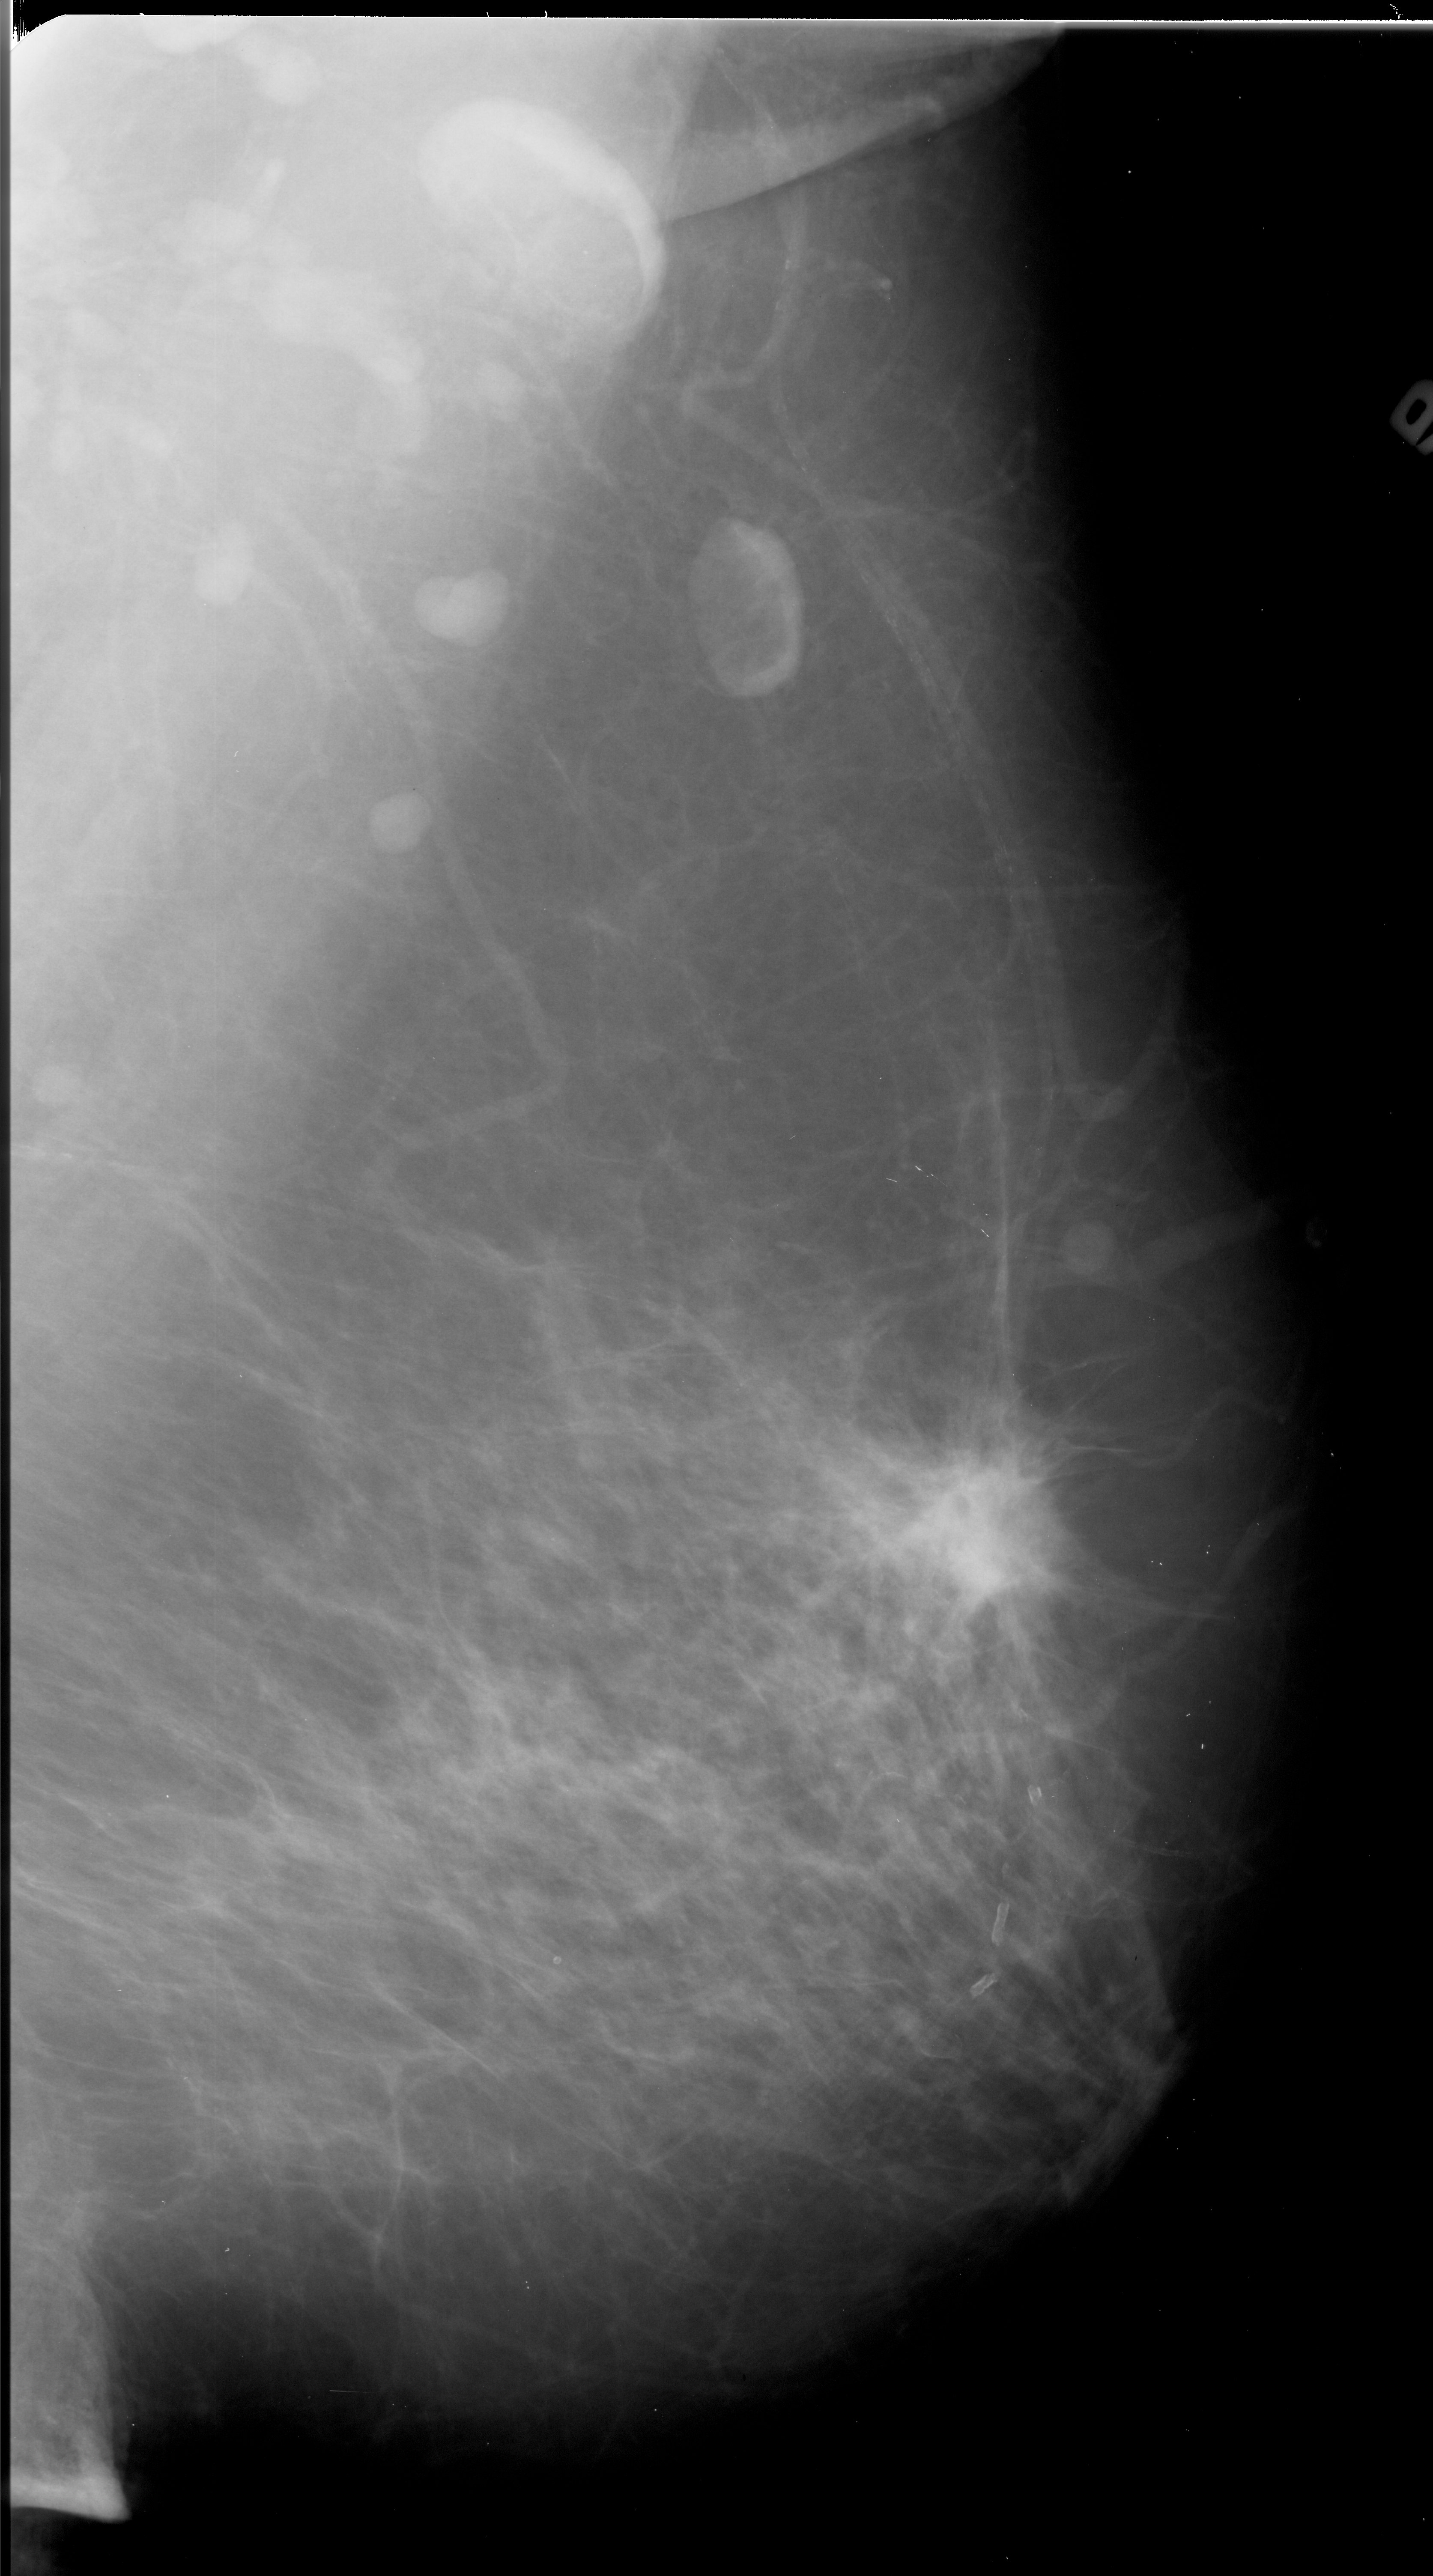
Mammogram (digitized film), right breast, mediolateral oblique (MLO) view, BI-RADS breast density category 2 (scale 1–4).
Marked findings (only marked abnormalities are described; nothing is implied about the rest of the image): mass, shape irregular, margins spiculated; BI-RADS assessment category 5; subtlety rating 5 on a 1 (subtle) to 5 (obvious) scale; pathology result (as recorded, not read from the image): malignant.